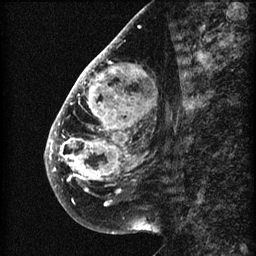
Breast MRI (dynamic contrast-enhanced), one sagittal slice; slice 24 of 60 in the series (ordered by position); 3 images stored at this slice position (order not interpretable as contrast timing); 1.5 T; TE 4.2 ms, TR 22.7 ms; 2 mm slice thickness; 256 × 256 image matrix, field of view 180 × 180 mm. Patient: female, 48 years. Case-level facts recorded for this patient, not image findings: setting: breast cancer imaged before/during neoadjuvant chemotherapy; receptor status: triple-negative.
Structures marked on this image (semi-automatic segmentation, software-assisted and operator-edited):
- analysis volume of interest (the breast-tissue region the enhancement analysis was run in; not a lesion): bounding box [x1, y1, x2, y2] px = [45, 30, 173, 207]
- tumour enhancement mask (voxels above the 90 % enhancement threshold inside the analysis volume of interest): [46, 40, 137, 192]